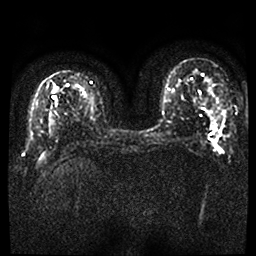
Breast MRI, one axial slice. Position 19 of 50 along the scan axis. Diffusion-weighted series; image 2 of 4 stored at this slice position (different b-values; order by instance number). 1.5 T. 4 mm slice thickness. 256 × 256 image matrix, field of view 340 × 340 mm. Female patient.
Annotated regions visible in this slice (outlined manually by an expert reader):
- tumour on diffusion-weighted imaging: box from (x=213, y=129) to (x=224, y=153) px